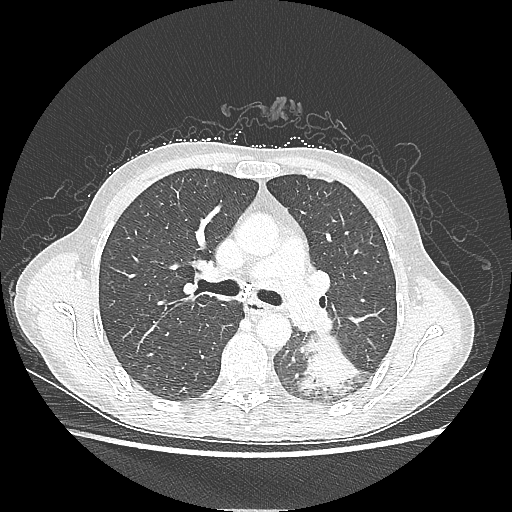
Chest CT, one axial slice. Slice 136 of 220 in the series (ordered by position). Reconstruction kernel LUNG. Lung window (W 1500 / L -600 HU). 512 × 512 image matrix. Female patient, age 53 years. From the clinical record (not read from this slice): clinical TNM (as recorded): T3 N0 M0.
Outlined on this slice (bounding box drawn by a radiologist):
- lung tumour (recorded histology: adenocarcinoma): bounding box <295,336,360,398> (left, top, right, bottom; pixels)